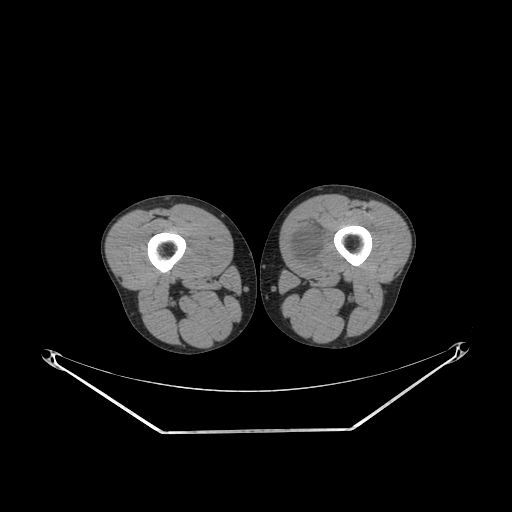
CT of an extremity soft-tissue mass (from a PET/CT study), one axial slice; position 232 of 311 along the scan axis; reconstruction kernel SOFT; 140 kVp; soft-tissue window (W 400 / L 40 HU); 3.75 mm slice thickness; 512 × 512 image matrix, field of view 500 × 500 mm. Male patient. From the clinical record (not read from this slice): histological type: mixoid liposarcoma; grade: low; site of the primary tumour: left thigh.
Structures marked on this image (expert contour drawn on MRI and transferred to this co-registered scan by the dataset authors):
- gross tumour volume (mass): box from (x=285, y=224) to (x=327, y=275) px